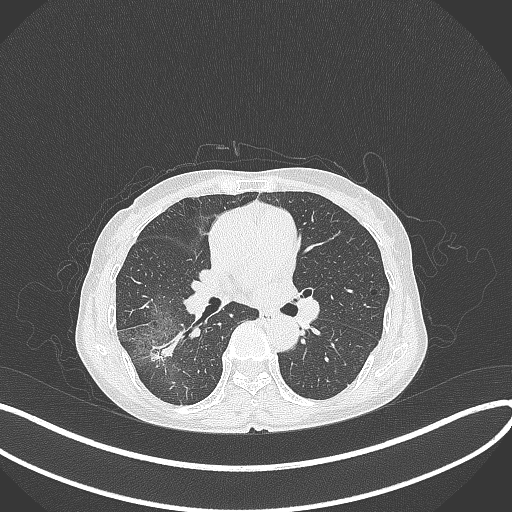
Chest CT, one axial slice. Reconstruction kernel B70f. 120 kVp. Lung window (W 1500 / L -600 HU). 512 × 512 image matrix, field of view 400 × 400 mm. Patient: female, 69 years. From the clinical record (not read from this slice): clinical TNM (as recorded): T1b N0 M0.
Outlined on this slice (rectangle marked by the reading radiologist):
- lung tumour (recorded histology: adenocarcinoma): bounding box (x1, y1, x2, y2) in pixels: (144, 330, 183, 364)